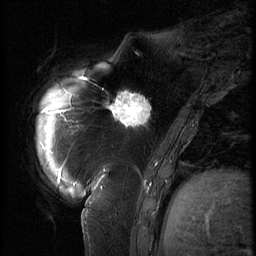
Breast MRI (dynamic contrast-enhanced), one sagittal slice; slice 17 of 62 in the series (ordered by position); 3 images stored at this slice position (order not interpretable as contrast timing); 1.5 T; TE 4.2 ms, TR 9 ms; 256 × 256 image matrix, field of view 180 × 180 mm. Female patient, age 57 years. From the clinical record (not read from this slice): setting: breast cancer imaged before/during neoadjuvant chemotherapy; receptor status: triple-negative.
Structures marked on this image (semi-automatic segmentation, software-assisted and operator-edited):
- analysis volume of interest (the breast-tissue region the enhancement analysis was run in; not a lesion): bounding box [x1, y1, x2, y2] px = [105, 84, 158, 135]
- tumour enhancement mask (voxels above the 140 % enhancement threshold inside the analysis volume of interest): [110, 90, 152, 127]